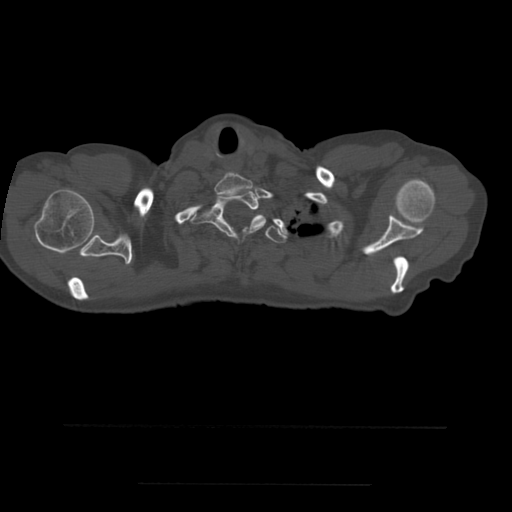
CT including the spine, one axial slice; bone window (W 1800 / L 400 HU); 1.25 mm slice thickness; 512 × 512 image matrix. Patient age 58 years. From the clinical record (not read from this slice): primary cancer: lung.
Structures marked on this image (semi-automatically segmented with operator editing):
- T1 vertebra: box from (x=191, y=189) to (x=262, y=237) px
- T2 vertebra: (x=242, y=215)–(x=287, y=243)